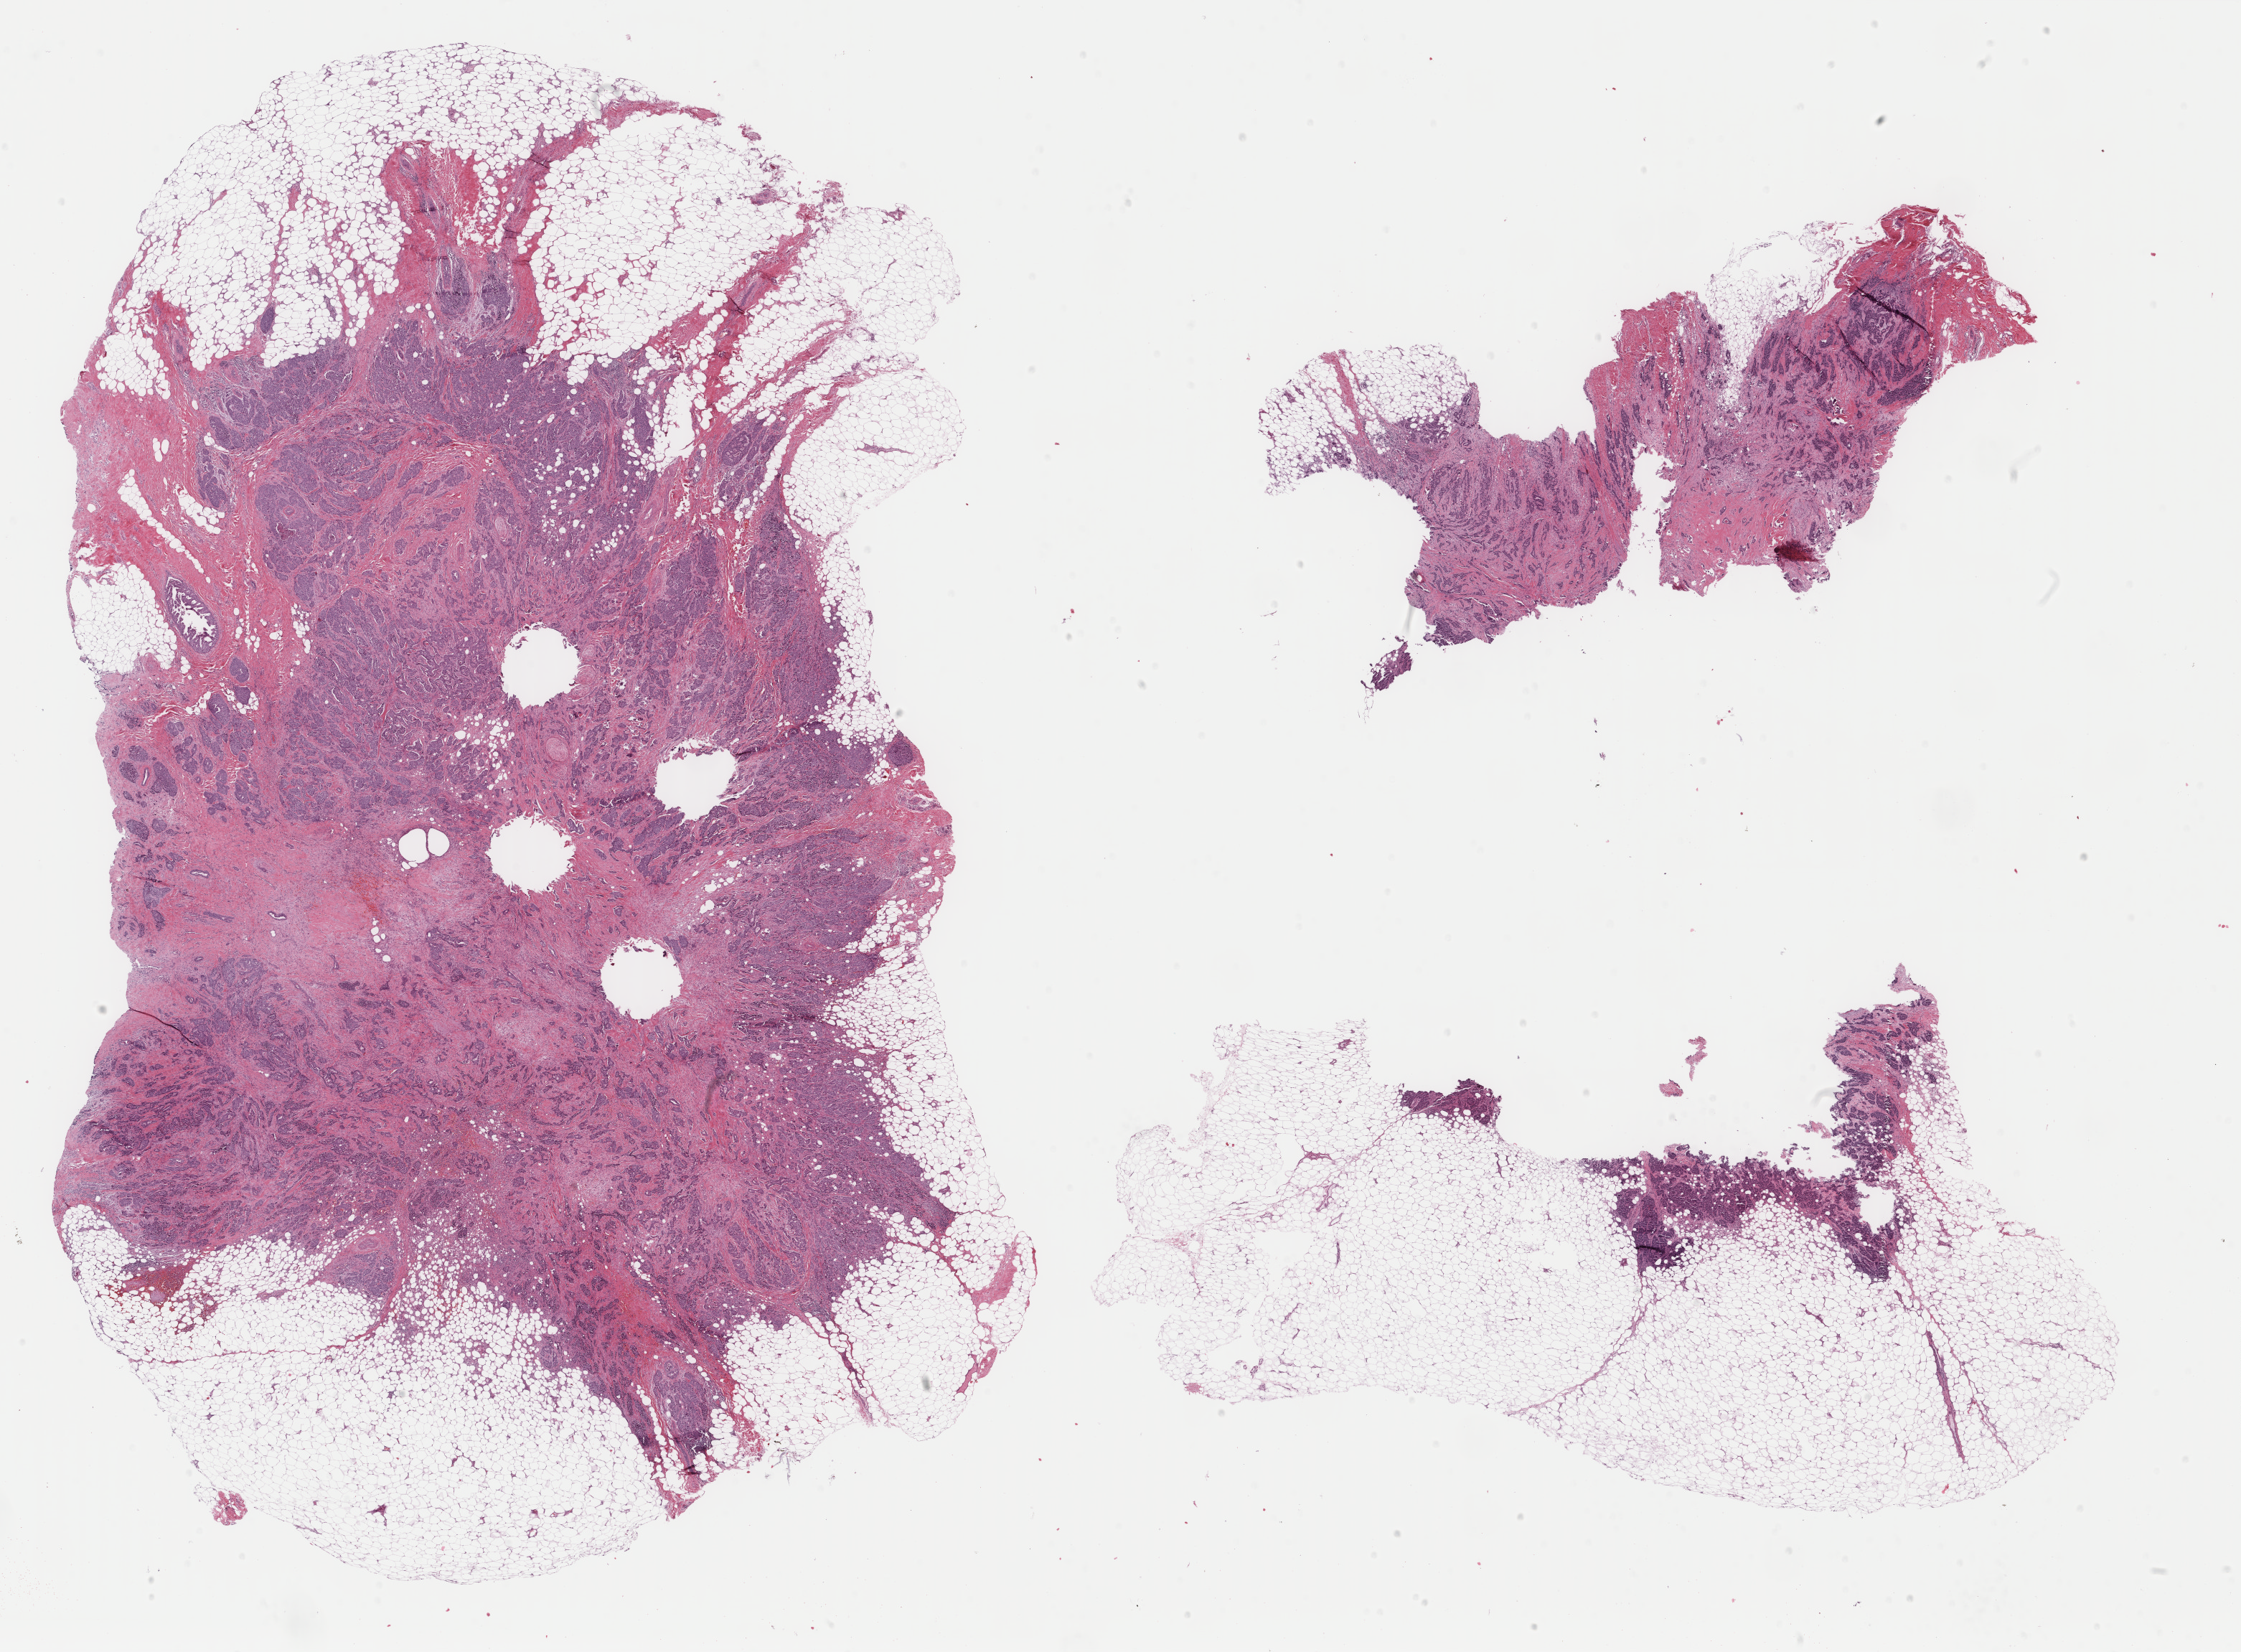
Hematoxylin and eosin (H&E) stained whole-slide image, shown as a low-resolution overview of the whole scanned area (about 24.8 x 18.3 mm), FFPE section, primary tumour sample from the breast. Female, age 61 years at initial diagnosis.
Lymph nodes positive (case pathology): 0 of 4 examined. AJCC pathologic stage: I (6th edition). TNM: T1 N0 M0. Pathologic diagnosis: Infiltrating duct carcinoma, NOS.